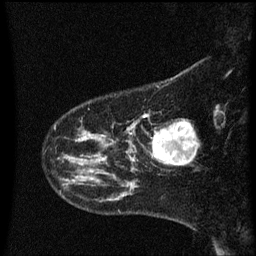
Breast MRI (dynamic contrast-enhanced), one sagittal slice. Position 11 of 60 along the scan axis. Dynamic contrast-enhanced series, image 2 of 3 at this slice position (ordered by acquisition). 1.5 T. TE 4.2 ms, TR 8.4 ms. 2 mm slice thickness. 256 × 256 image matrix. Female patient, age 41 years. From the clinical record (not read from this slice): setting: breast cancer imaged before/during neoadjuvant chemotherapy; receptor status: triple-negative.
Outlined on this slice (semi-automatically segmented with operator editing):
- analysis volume of interest (the breast-tissue region the enhancement analysis was run in; not a lesion): box from (x=141, y=116) to (x=197, y=165) px
- tumour enhancement mask (voxels above the 70 % enhancement threshold inside the analysis volume of interest): (x=153, y=122)–(x=196, y=165)